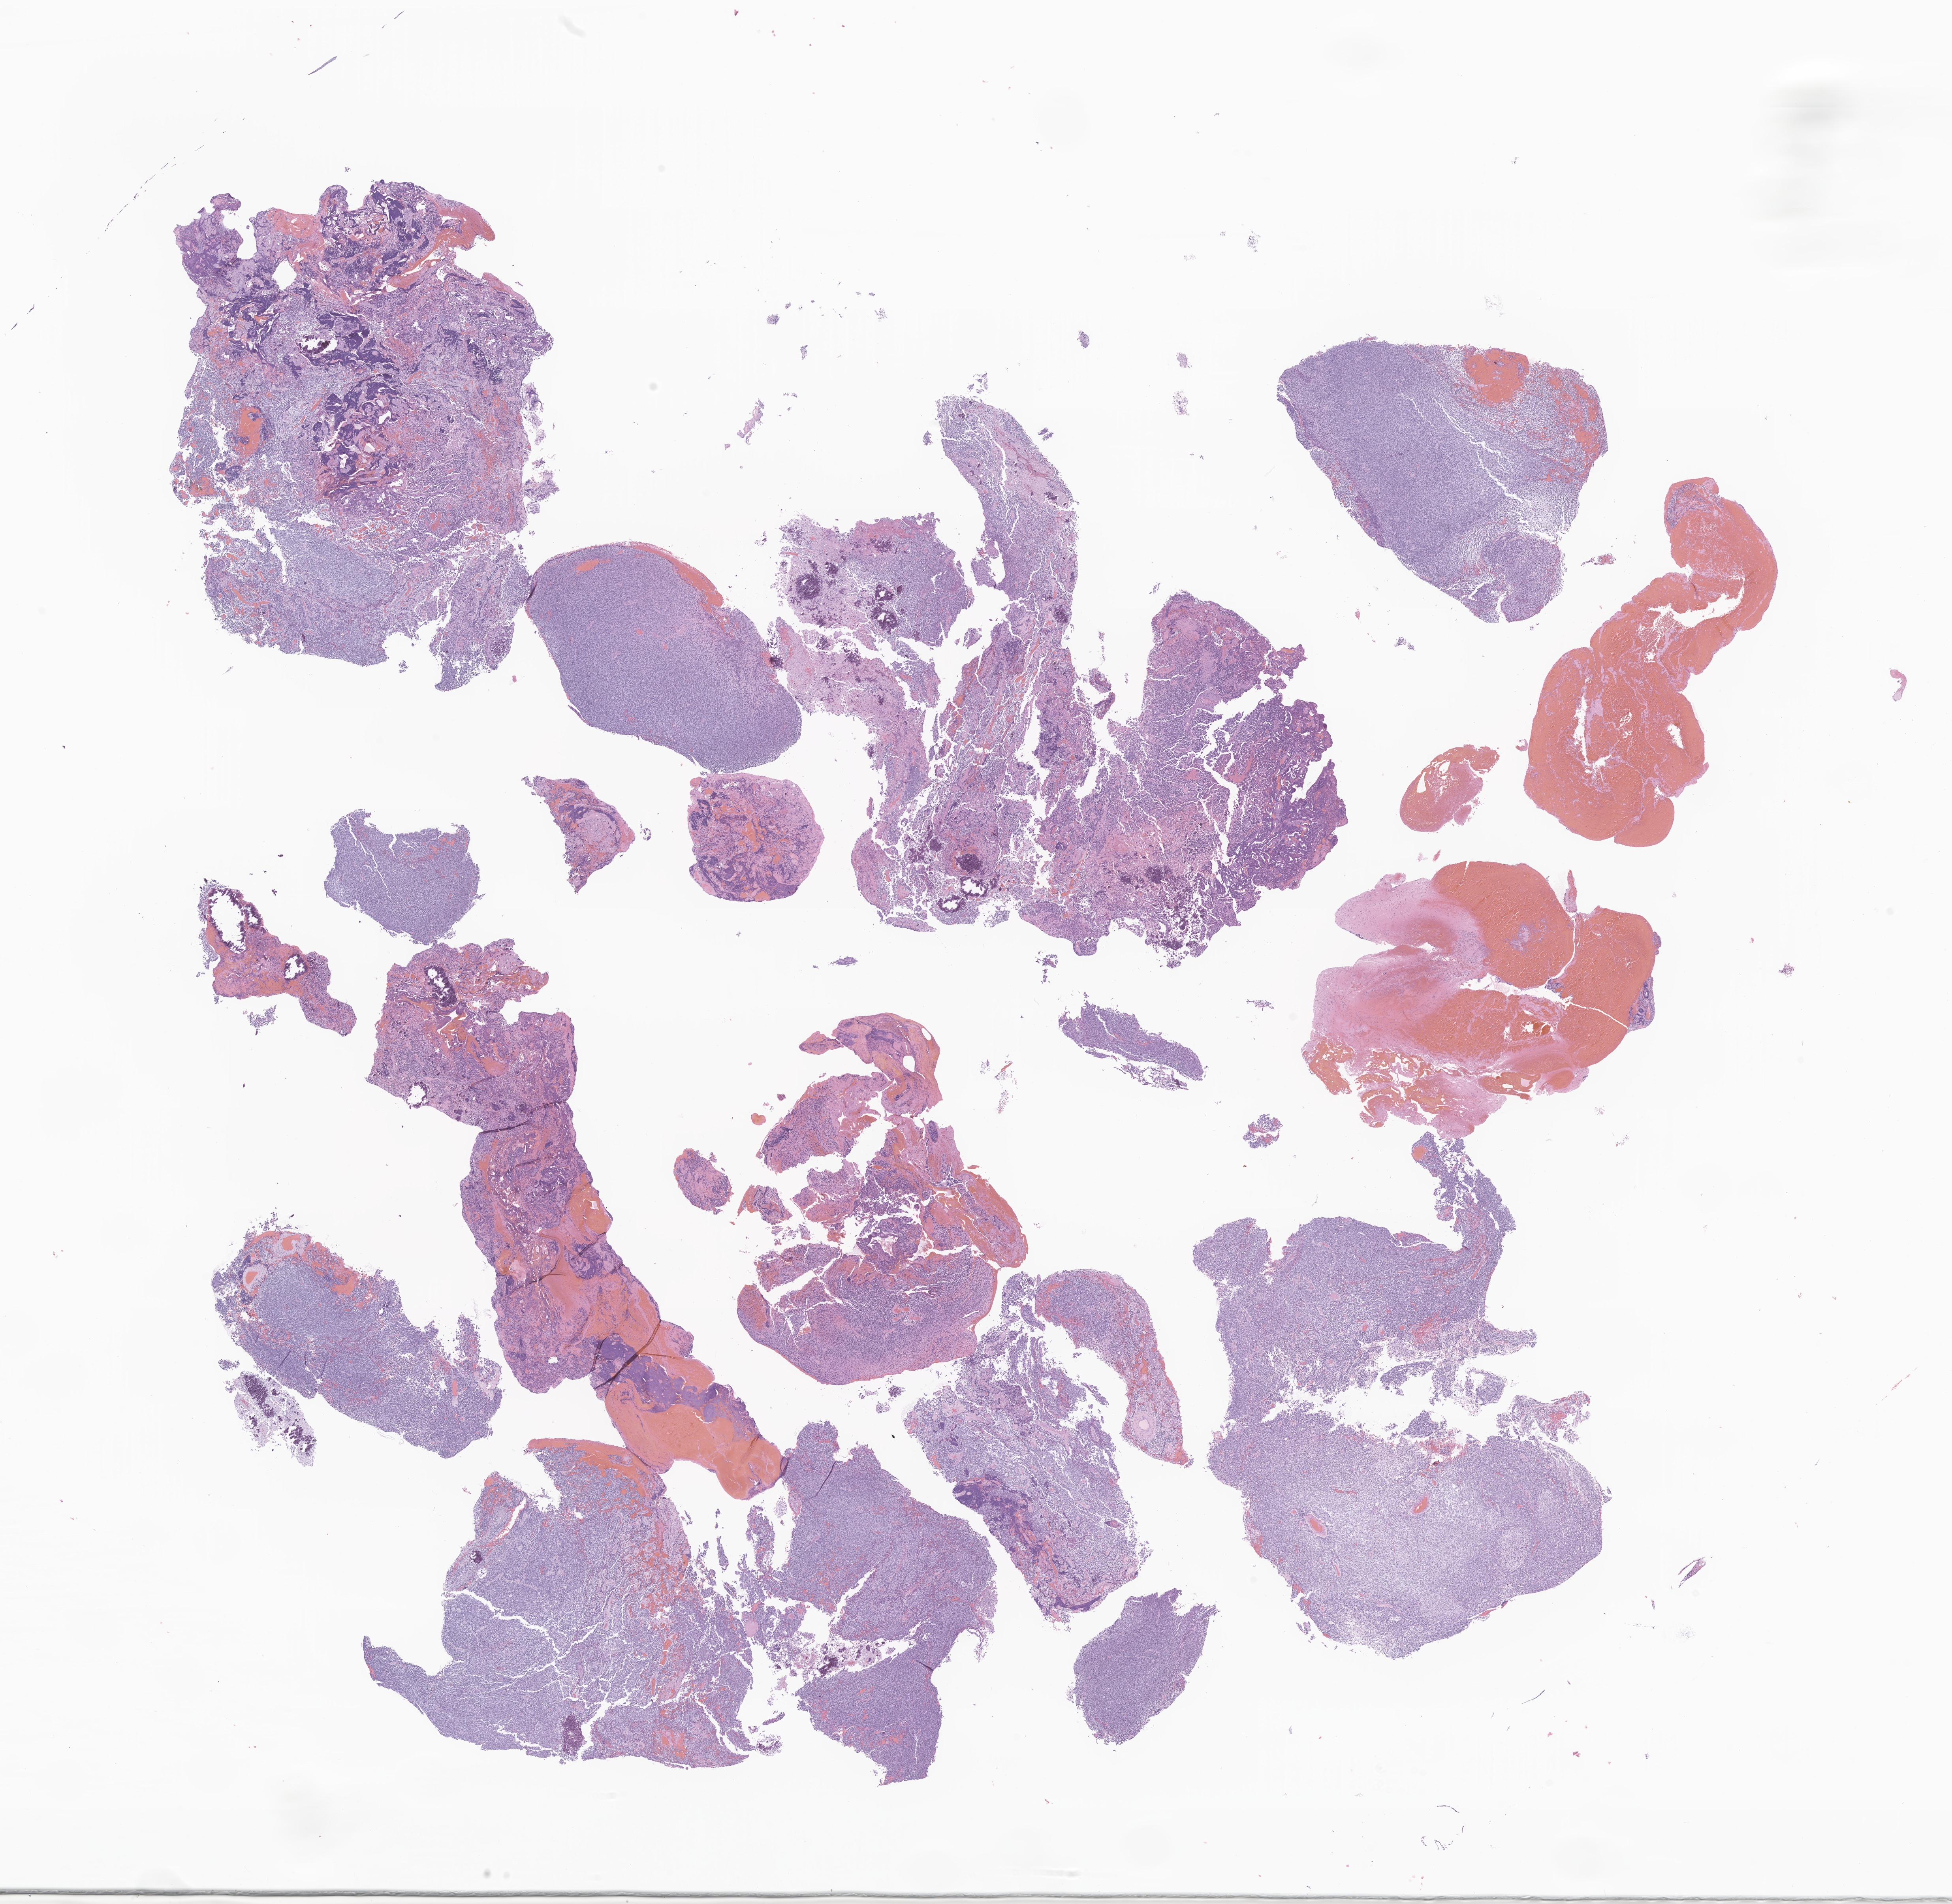
Whole-slide image, H&E stain of tumor tissue from the brain, shown as a low-resolution overview of the whole scanned area (about 20.8 x 20.3 mm), formalin-fixed paraffin-embedded section. Male patient, age 81 months.
Diagnosis (ICD-O-3 morphology term): Medulloblastoma, NOS.